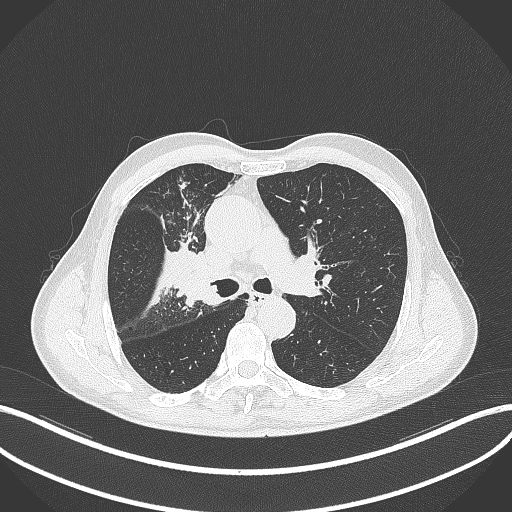
Chest CT, one axial slice. Position 310 of 490 along the scan axis. Lung window (W 1500 / L -600 HU). 512 × 512 image matrix, field of view 400 × 400 mm. Patient: male, 69 years. Case-level facts recorded for this patient, not image findings: clinical TNM (as recorded): T2a N0 M0.
Outlined on this slice (bounding box drawn by a radiologist):
- lung tumour (recorded histology: adenocarcinoma): box from (x=172, y=238) to (x=223, y=307) px